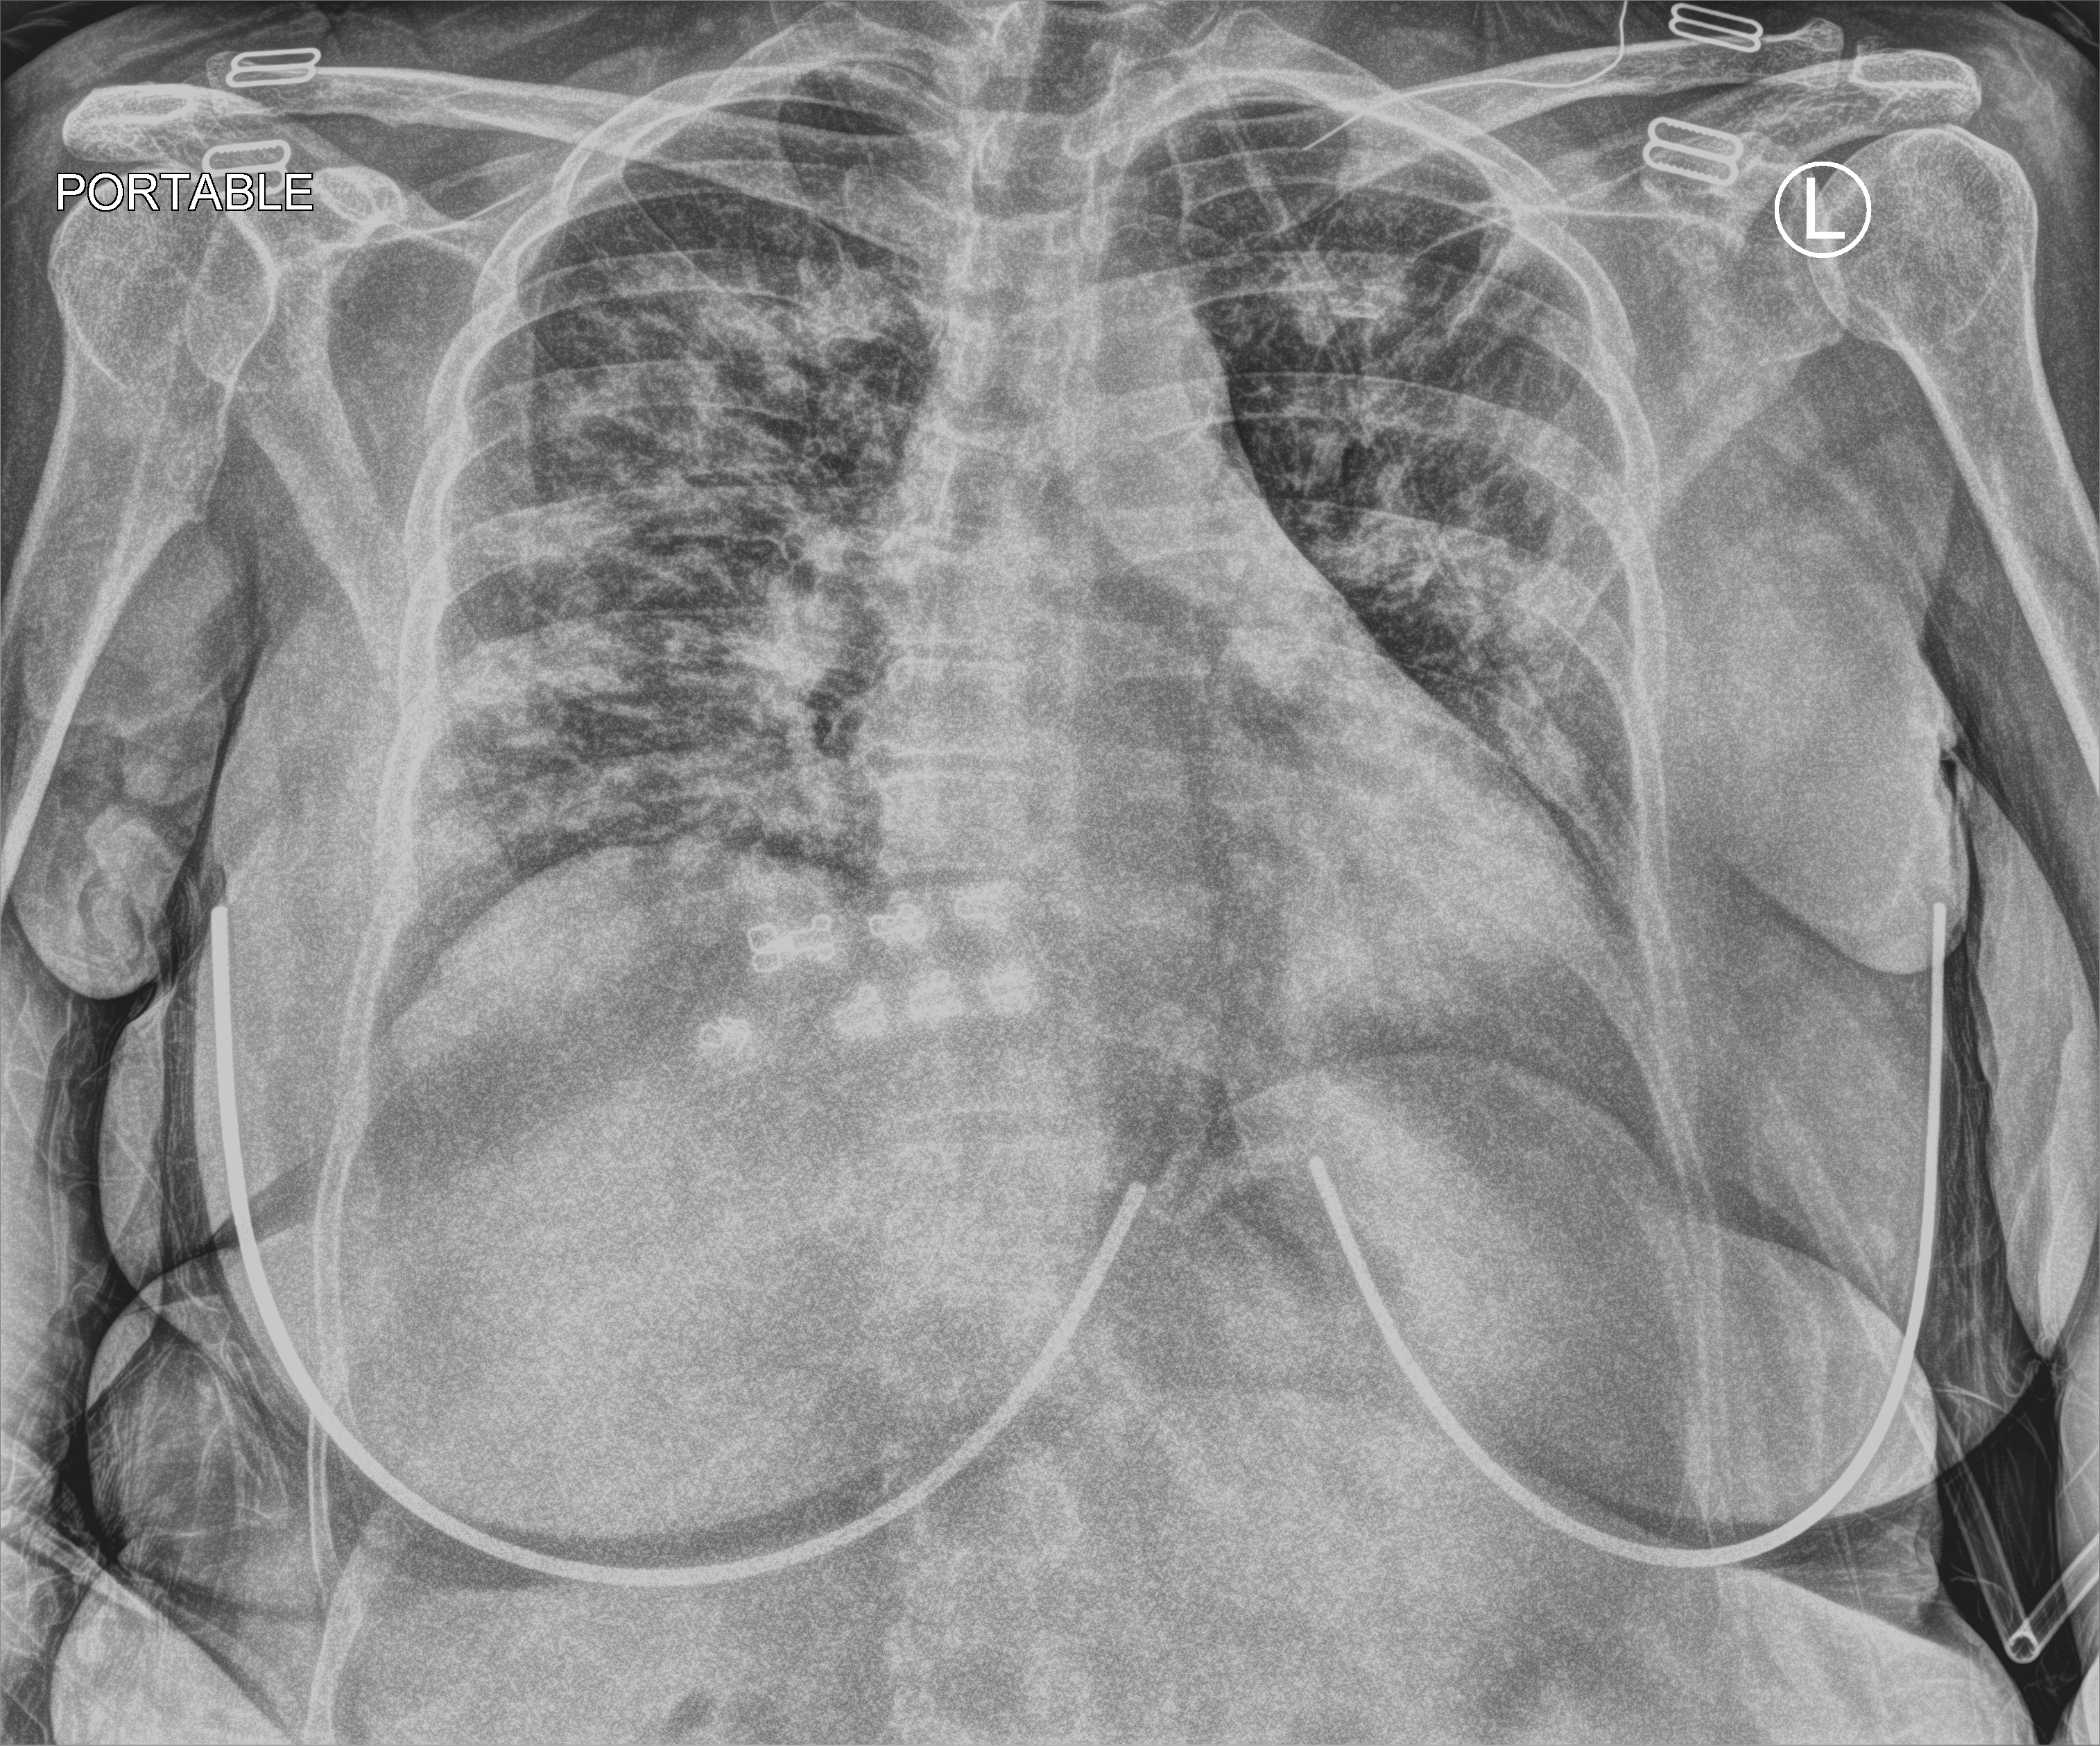
Portable chest radiograph, anteroposterior (AP) projection. Female patient hospitalised with COVID-19, age 60–74 years.
Hospital-stay facts (about this admission, not read from this image; timing relative to this image not recorded):
- hypertension (admission record): yes
- mechanically ventilated during this hospital stay: no